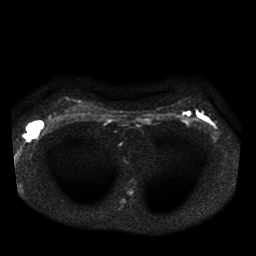
Breast MRI, one axial slice. Diffusion-weighted series; image 2 of 4 stored at this slice position (different b-values; order by instance number). 1.5 T. 5 mm slice thickness. 256 × 256 image matrix, field of view 330 × 330 mm. Female patient.
Outlined on this slice (expert manual segmentation):
- tumour on diffusion-weighted imaging: bounding box (x1, y1, x2, y2) in pixels: (27, 124, 37, 137)